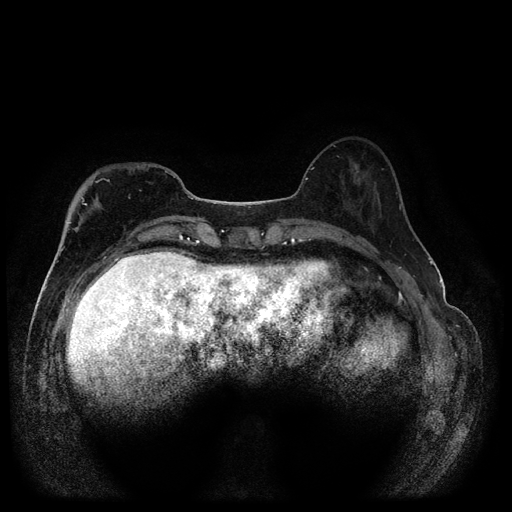
Breast MRI (dynamic contrast-enhanced, multi-phase), one axial slice. Slice 35 of 116 in the series (ordered by position). Dynamic contrast-enhanced series, time point 2 of 5 at this slice position (early post-contrast). 1.5 T. TE 2.6 ms, TR 5.4 ms. 2 mm slice thickness. 512 × 512 image matrix. Patient: female, 51 years.
Structures marked on this image (semi-automatically segmented with operator editing):
- breast lesion (labelled benign in the annotation): bounding box [x1, y1, x2, y2] px = [353, 164, 360, 175]